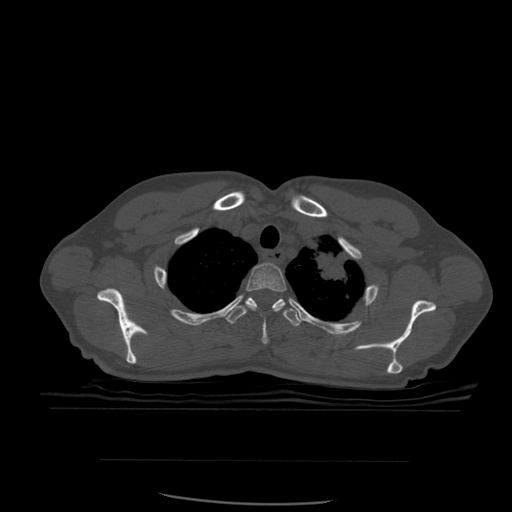
CT including the spine, one axial slice; position 450 of 574 along the scan axis; bone window (W 1800 / L 400 HU); 512 × 512 image matrix, field of view 392 × 392 mm. Patient age 48 years. From the clinical record (not read from this slice): primary cancer: lung.
Structures marked on this image (semi-automatic segmentation, software-assisted and operator-edited):
- T2 vertebra: bounding box [x1, y1, x2, y2] px = [246, 263, 287, 344]
- T3 vertebra: [226, 297, 302, 327]